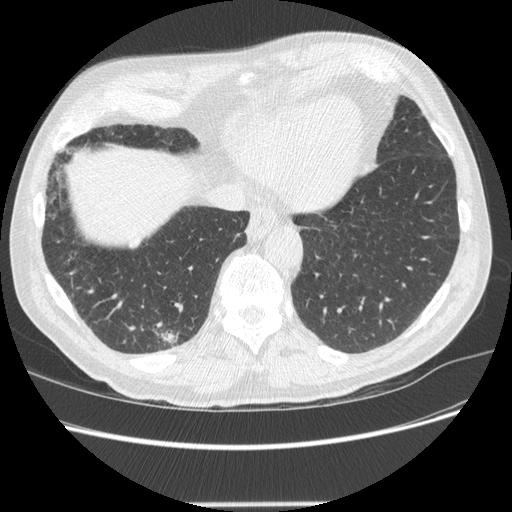
Low-dose screening chest CT, one axial slice. Slice 58 of 245 in the series (ordered by position). Reconstruction kernel STANDARD. 120 kVp. Lung window (W 1500 / L -600 HU). 512 × 512 image matrix.
Annotated regions visible in this slice (manually delineated by an expert):
- lesion 1 (tumor, lower lobe of right lung): box from (x=160, y=331) to (x=177, y=345) px